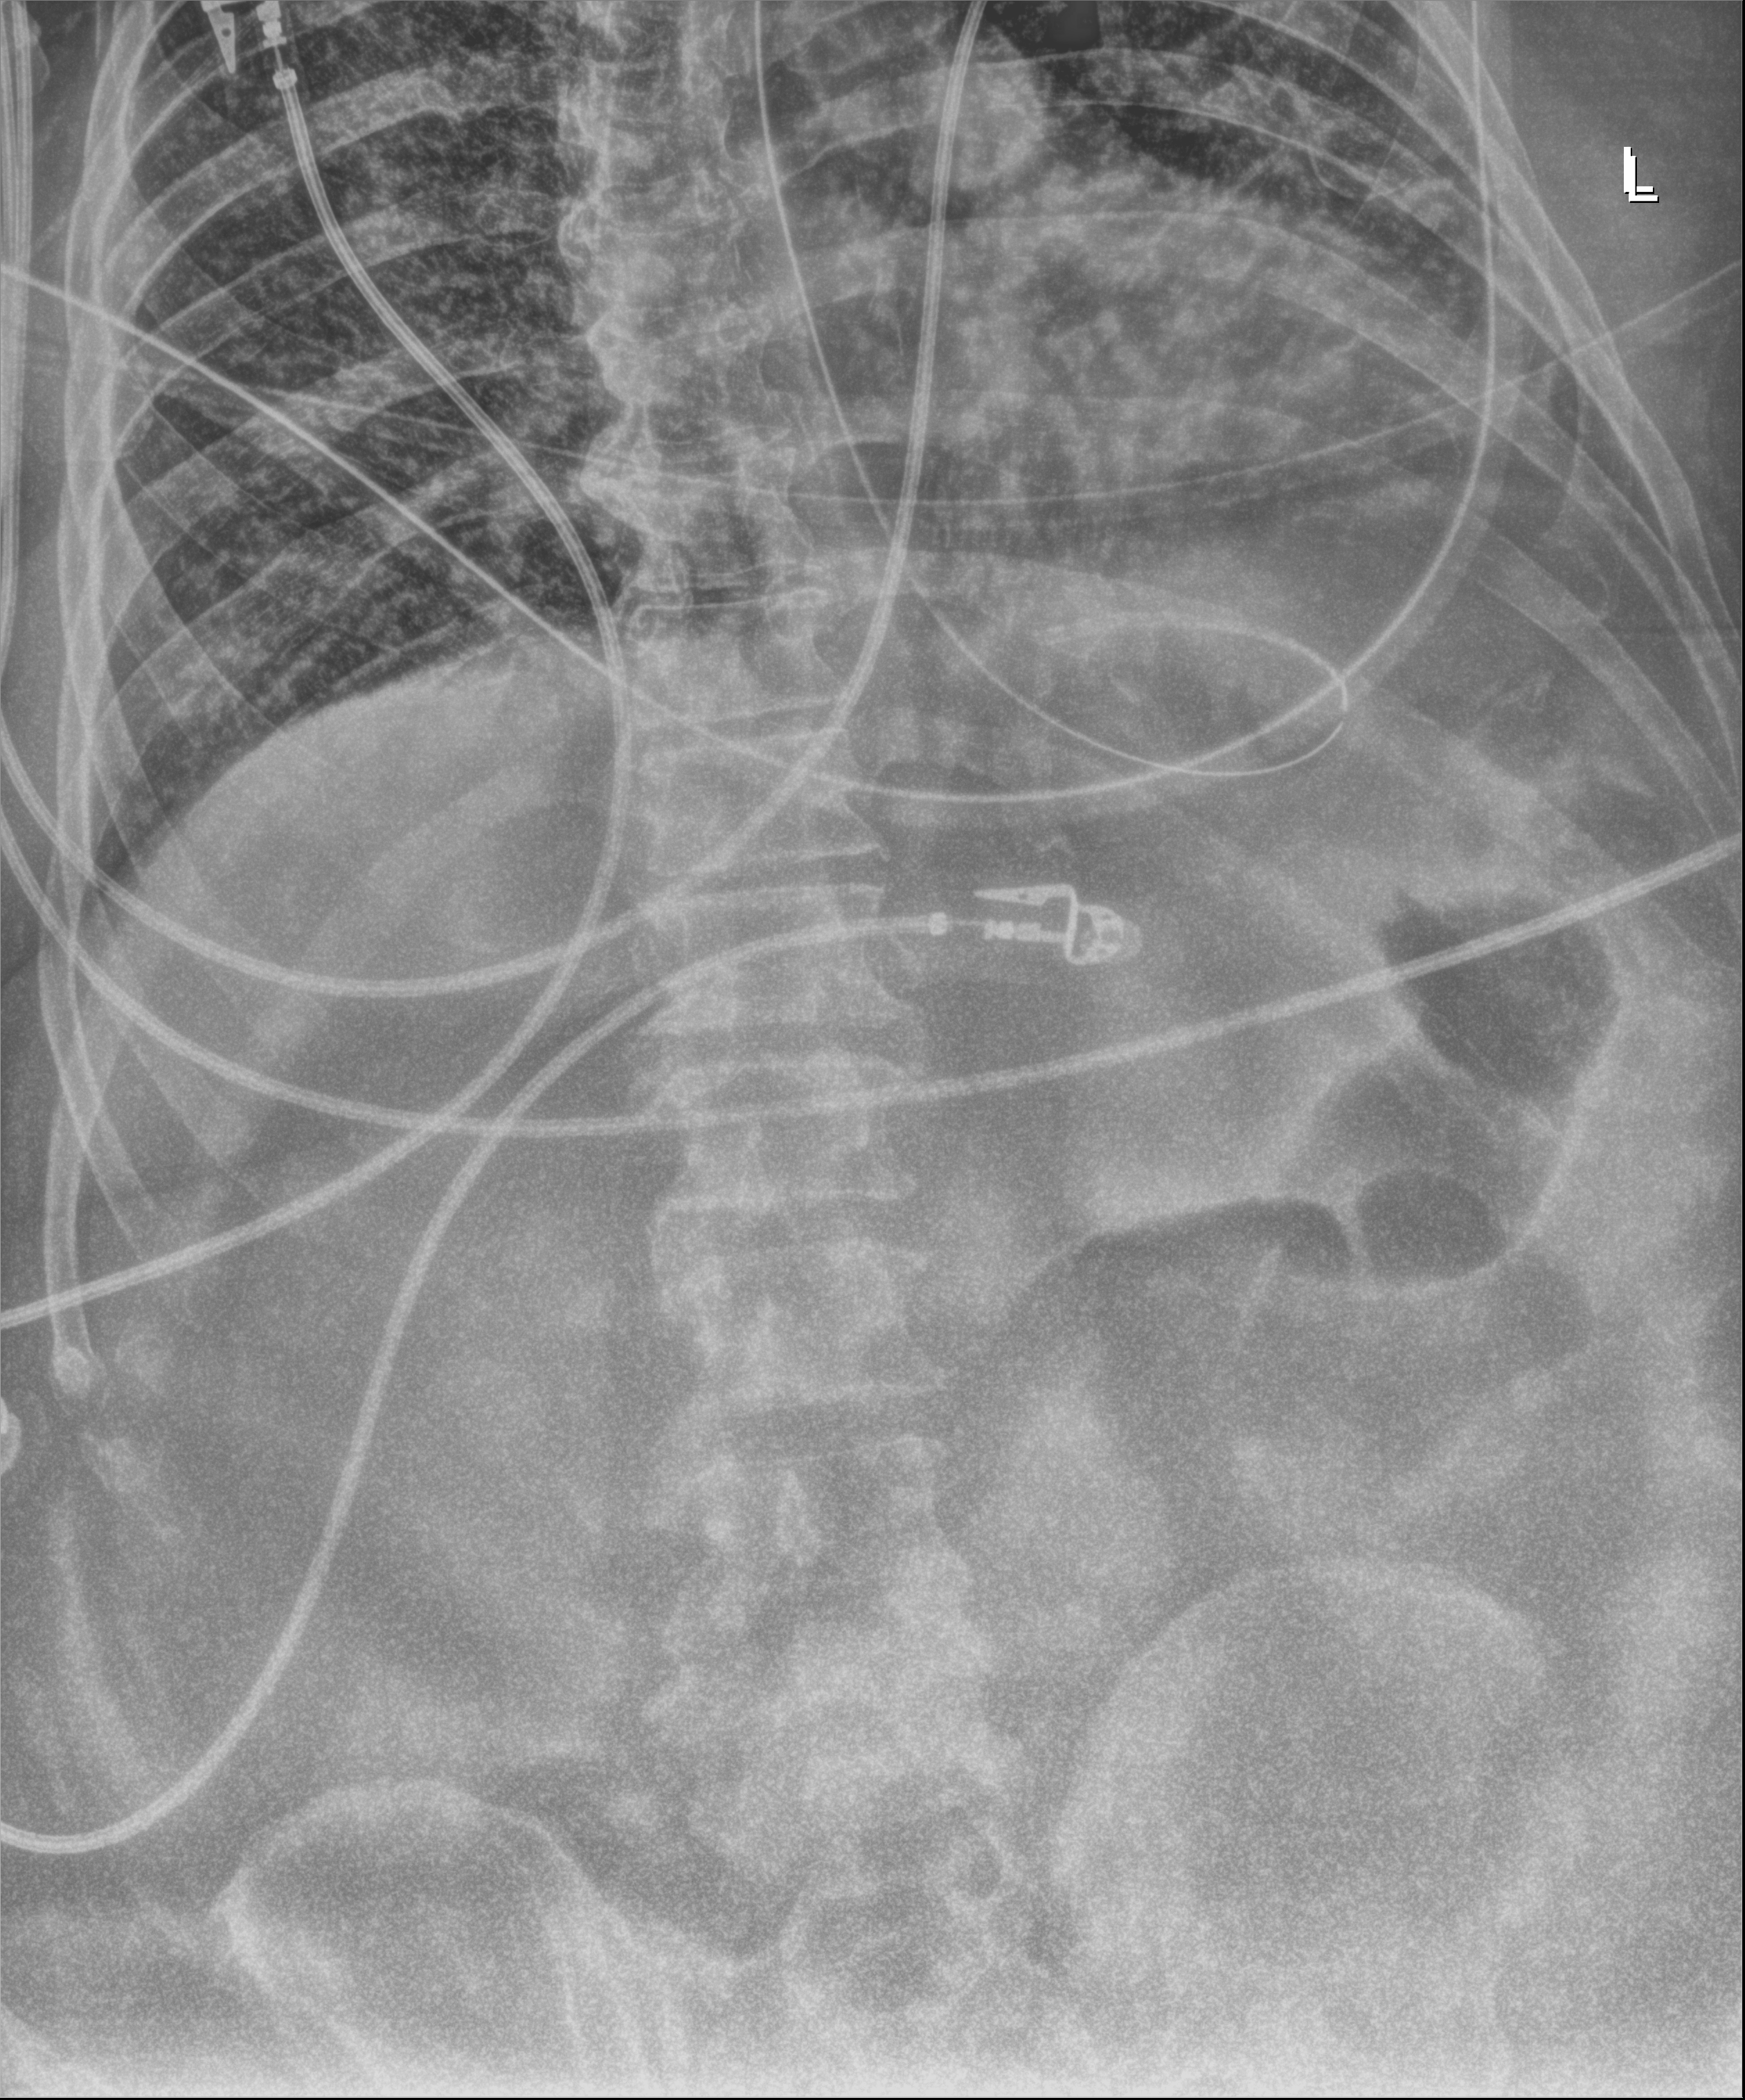
Portable abdomen radiograph; anteroposterior (AP) projection. Adult patient hospitalised with COVID-19, age 18–59 years.
From the hospital-stay record, not from the radiograph (when in the stay this image was taken is not recorded): admitted to intensive care during this hospital stay: yes; length of hospital stay: 28 days; mechanically ventilated during this hospital stay: yes.